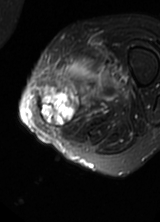
MRI of an extremity soft-tissue mass, one axial slice. T2-weighted fat-saturated. MR volume resampled by the dataset authors to the PET/CT grid (not the native acquisition matrix). 3.27 mm slice thickness. 160 × 222 image matrix, field of view 156 × 217 mm. Female patient. From the clinical record (not read from this slice): histological type: pleomorphic leiomyosarcoma; grade: high; site of the primary tumour: left thigh.
Outlined on this slice (expert contour drawn on MRI and transferred to this co-registered scan by the dataset authors):
- gross tumour volume including surrounding oedema: box from (x=38, y=54) to (x=126, y=130) px
- gross tumour volume (mass): (x=38, y=84)–(x=80, y=128)